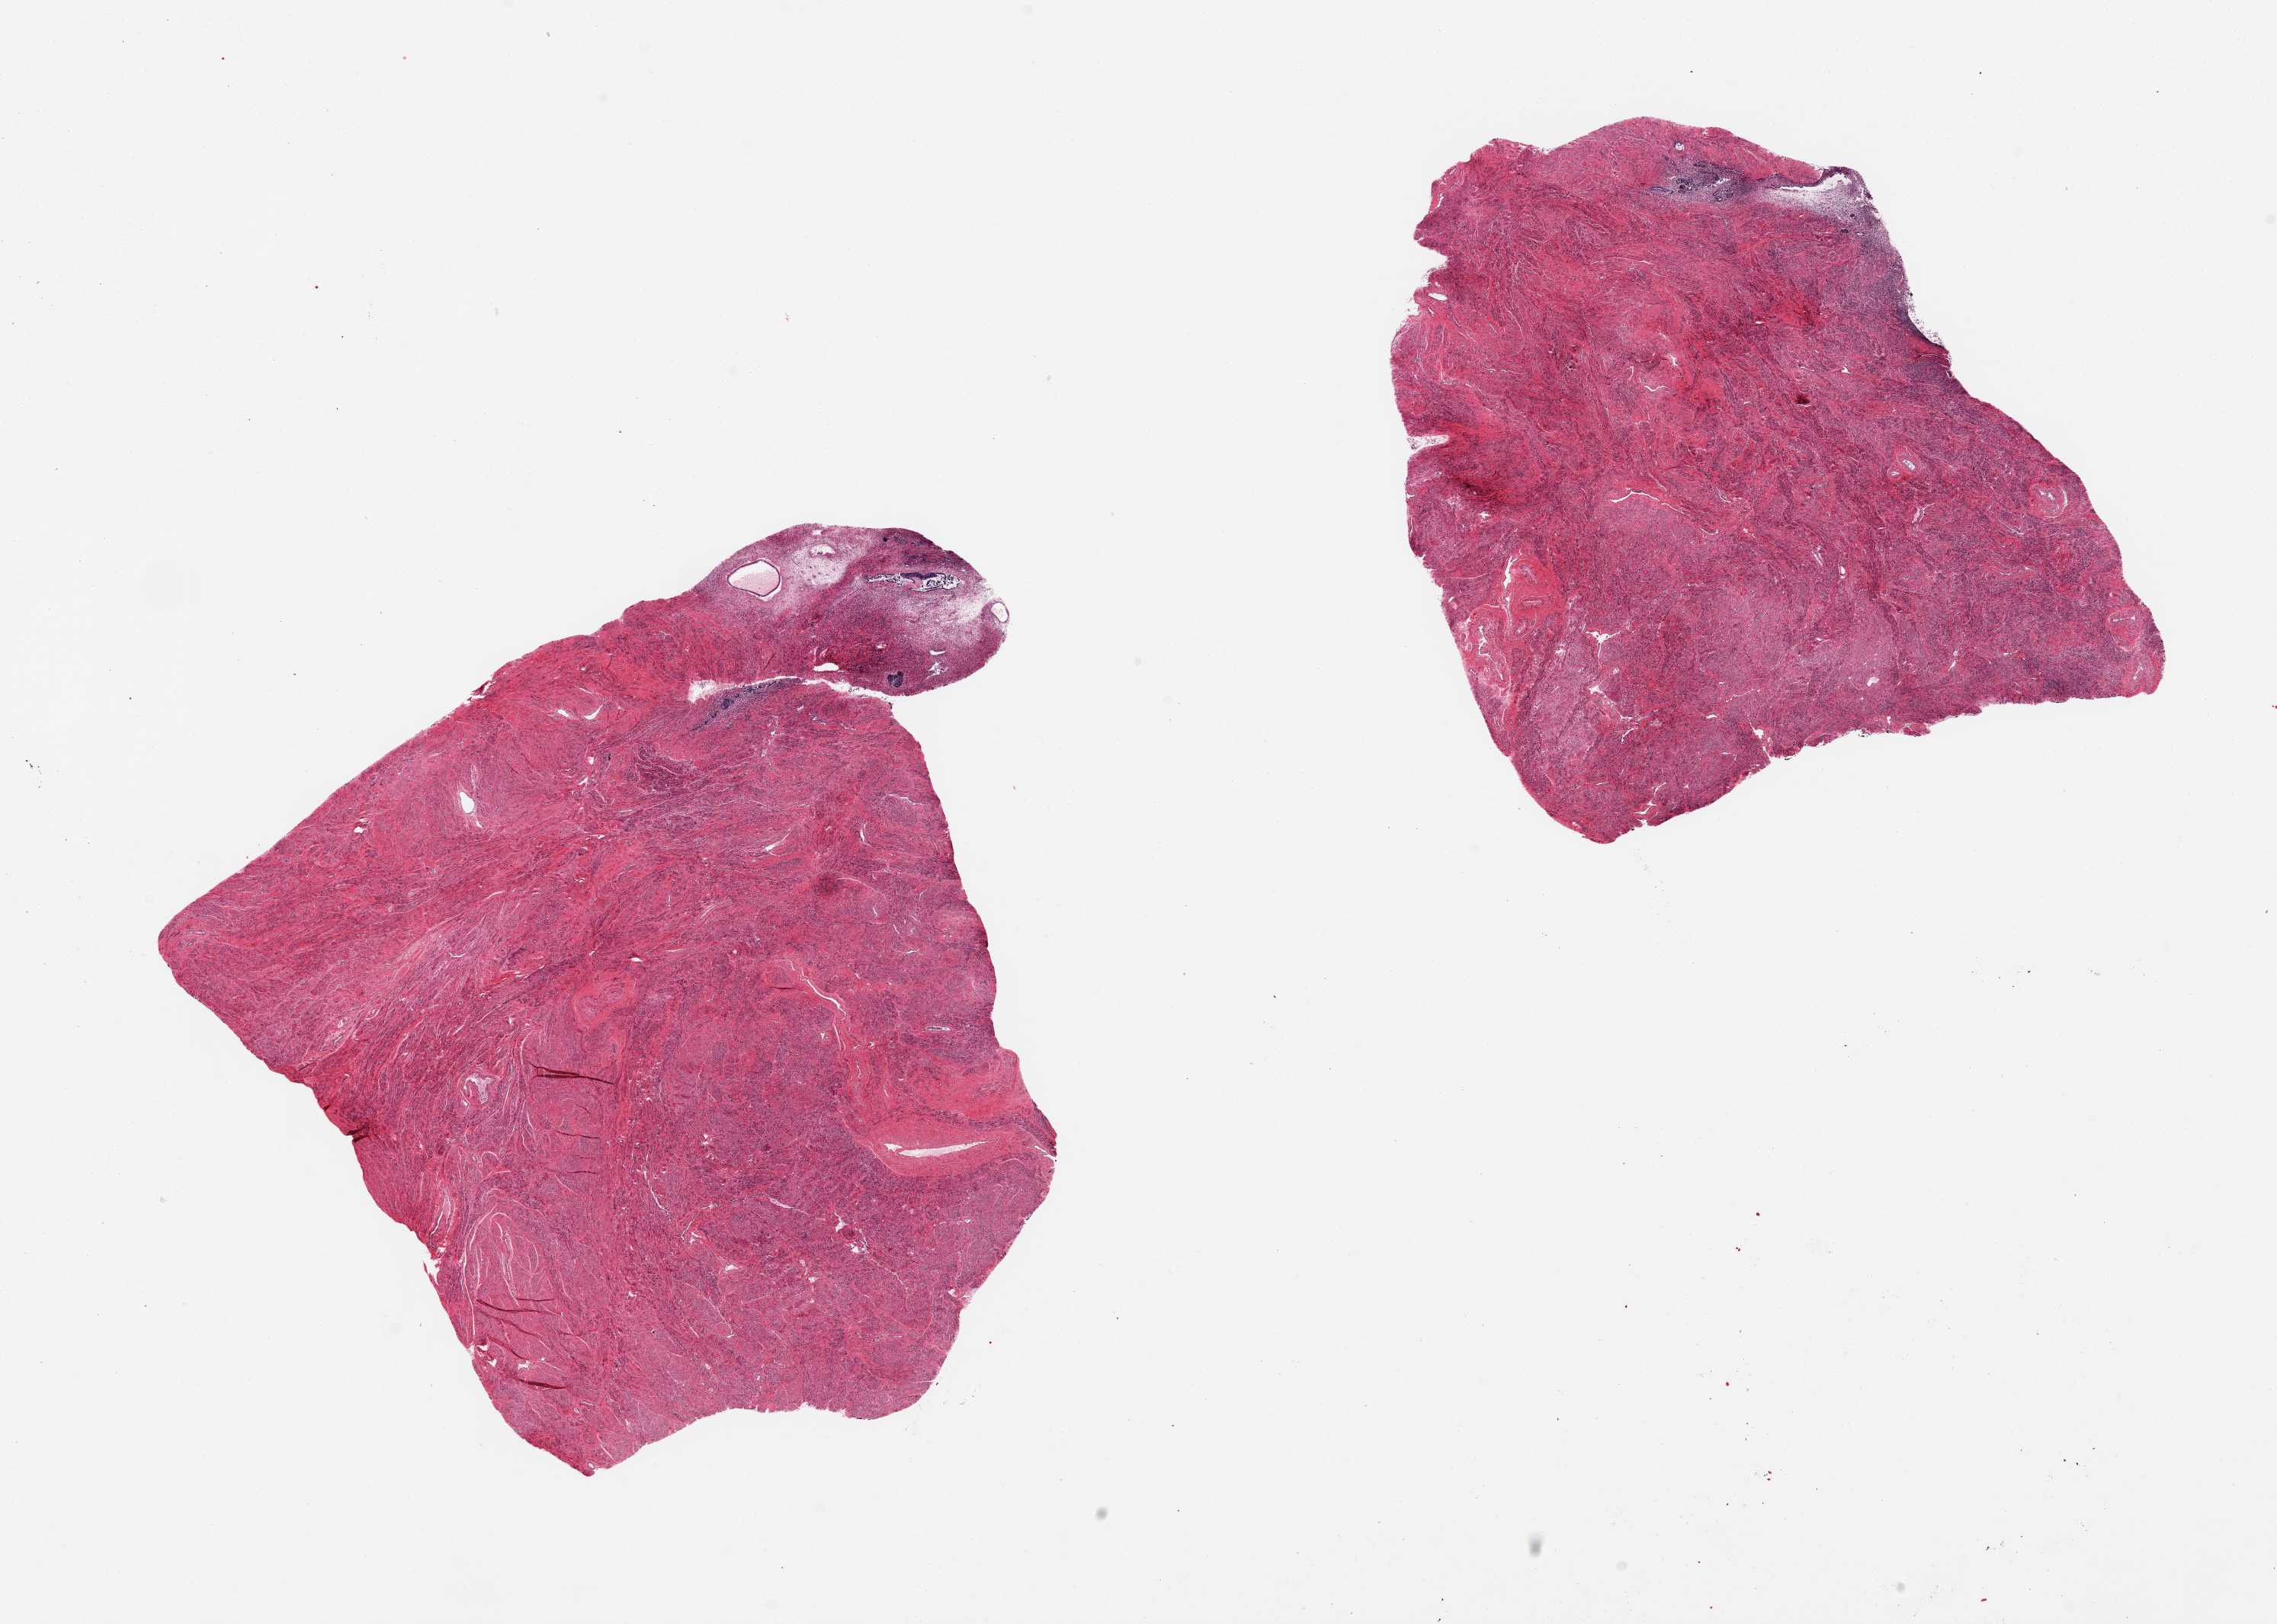
Whole-slide image, hematoxylin and eosin (H&E) stain, brightfield — low-resolution overview of the scanned area, about 23.6 x 16.9 mm (acquisition: 20x scan); PAXgene-fixed, paraffin-embedded tissue; sampled site (target tissue): uterus; tissue donor sample. Female donor.
Pathologist's review note for this sample: 2 pieces, predominantly myometrium, minimal endometrium, inactive.